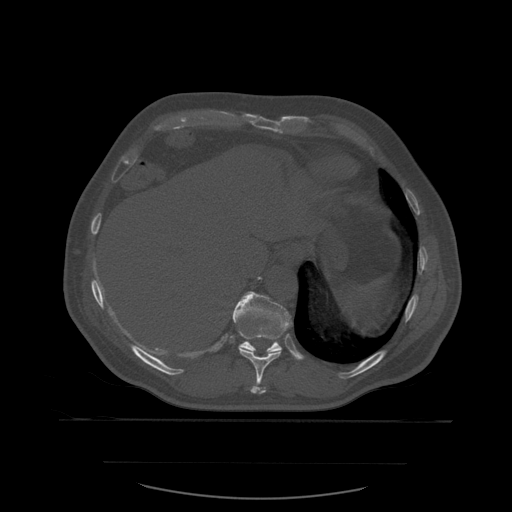
CT including the spine, one axial slice. Bone window (W 1800 / L 400 HU). 512 × 512 image matrix. Patient age 71 years. From the clinical record (not read from this slice): primary cancer: lung; vertebrae with lytic lesions (as recorded): T1, T2, L5, S1.
Outlined on this slice (semi-automatically segmented with operator editing):
- T10 vertebra: bounding box (x1, y1, x2, y2) in pixels: (233, 304, 289, 394)
- T11 vertebra: (233, 292, 293, 354)